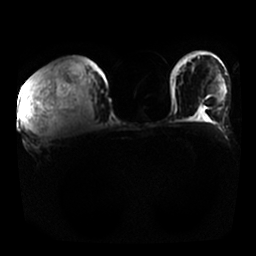
Breast MRI, one axial slice. Position 11 of 25 along the scan axis. Diffusion-weighted series; image 2 of 4 stored at this slice position (different b-values; order by instance number). 1.5 T. 4 mm slice thickness. 256 × 256 image matrix, field of view 350 × 350 mm. Female patient.
Annotated regions visible in this slice (manually delineated by an expert):
- tumour on diffusion-weighted imaging: bounding box <21,70,54,113> (left, top, right, bottom; pixels)